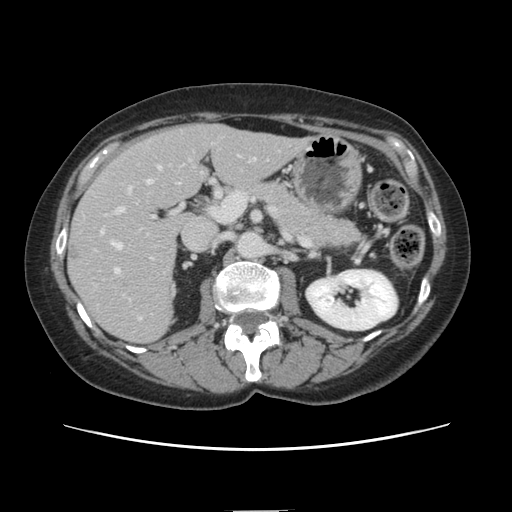
Contrast-enhanced abdominal CT, one axial slice; position 68 of 141 along the scan axis; intravenous contrast given; soft-tissue window (W 400 / L 40 HU); 2.5 mm slice thickness; 512 × 512 image matrix, field of view 350 × 350 mm. Female patient, age 63 years. From the clinical record (not read from this slice): diagnosis: colorectal cancer liver metastases, imaged before liver resection; multiple liver metastases: yes; largest metastasis: 3.2 cm; disease in both lobes: yes.
Structures marked on this image (expert manual segmentation):
- hepatic veins: bounding box <112,167,161,276> (left, top, right, bottom; pixels)
- liver: <69,125,306,342>
- planned liver remnant (the part of the liver to remain after resection): <175,125,308,192>
- portal vein (with intrahepatic branches): <101,186,141,319>
- liver metastasis: <120,281,127,288>
- liver metastasis: <68,244,80,261>